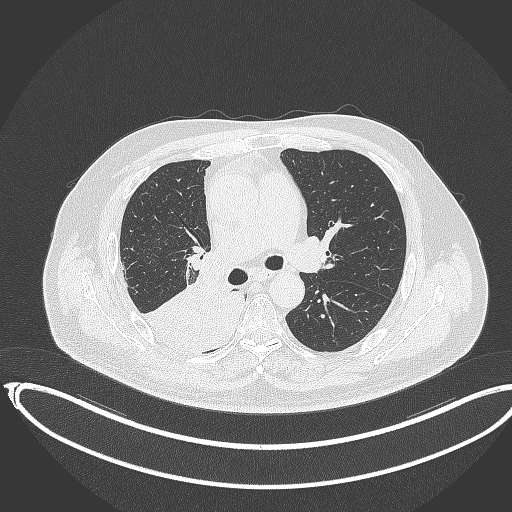
Chest CT, one axial slice. Slice 215 of 403 in the series (ordered by position). 120 kVp. Lung window (W 1500 / L -600 HU). 512 × 512 image matrix, field of view 436 × 436 mm. Patient: male, 68 years. Case-level facts recorded for this patient, not image findings: clinical TNM (as recorded): T2a N0 M0.
Outlined on this slice (bounding box drawn by a radiologist):
- lung tumour (recorded histology: adenocarcinoma): box from (x=146, y=279) to (x=244, y=353) px